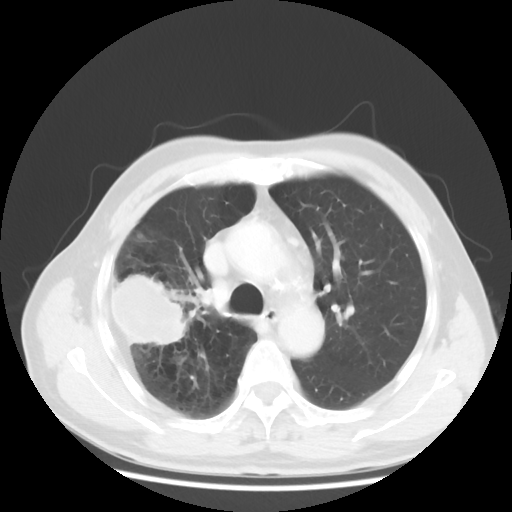
Chest CT, one axial slice. Position 34 of 50 along the scan axis. Reconstruction kernel STANDARD. Lung window (W 1500 / L -600 HU). 5 mm slice thickness. 512 × 512 image matrix. Male patient, age 69 years. From the clinical record (not read from this slice): clinical TNM (as recorded): T3 N0 M0.
Structures marked on this image (bounding box drawn by a radiologist):
- lung tumour (recorded histology: adenocarcinoma): bounding box [x1, y1, x2, y2] px = [114, 269, 193, 348]